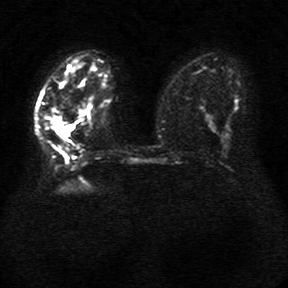
Breast MRI, one axial slice. Position 16 of 34 along the scan axis. Diffusion-weighted series; image 2 of 4 stored at this slice position (different b-values; order by instance number). 1.5 T. 288 × 288 image matrix, field of view 340 × 340 mm. Female patient.
Outlined on this slice (expert manual segmentation):
- tumour on diffusion-weighted imaging: box from (x=47, y=106) to (x=68, y=138) px